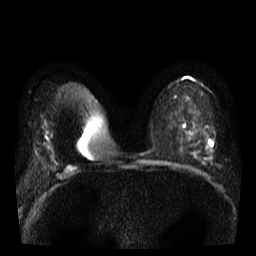
Breast MRI, one axial slice; slice 21 of 38 in the series (ordered by position); diffusion-weighted series; image 2 of 4 stored at this slice position (different b-values; order by instance number); 3 T; 5 mm slice thickness; 256 × 256 image matrix, field of view 320 × 320 mm. Female patient.
Structures marked on this image (outlined manually by an expert reader):
- tumour on diffusion-weighted imaging: bounding box [x1, y1, x2, y2] px = [204, 143, 213, 160]